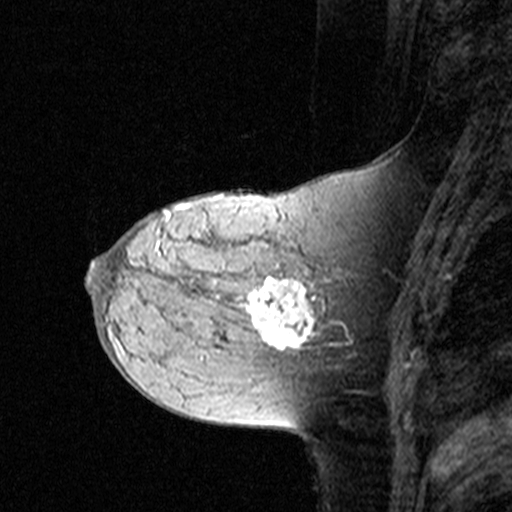
Breast MRI (dynamic contrast-enhanced), one sagittal slice. Position 15 of 44 along the scan axis. Dynamic contrast-enhanced study with each time point stored as its own series, time point 2 of 3 at this slice position (early post-contrast, ordered by acquisition time). 1.5 T. TE 4.5 ms, TR 11 ms. 3 mm slice thickness. 512 × 512 image matrix, field of view 200 × 200 mm. Patient: female, 44 years. From the clinical record (not read from this slice): setting: breast cancer imaged before/during neoadjuvant chemotherapy; receptor status: triple-negative.
Annotated regions visible in this slice (semi-automatically segmented with operator editing):
- analysis volume of interest (the breast-tissue region the enhancement analysis was run in; not a lesion): box from (x=142, y=208) to (x=349, y=363) px
- tumour enhancement mask (voxels above the 90 % enhancement threshold inside the analysis volume of interest): (x=249, y=278)–(x=349, y=349)